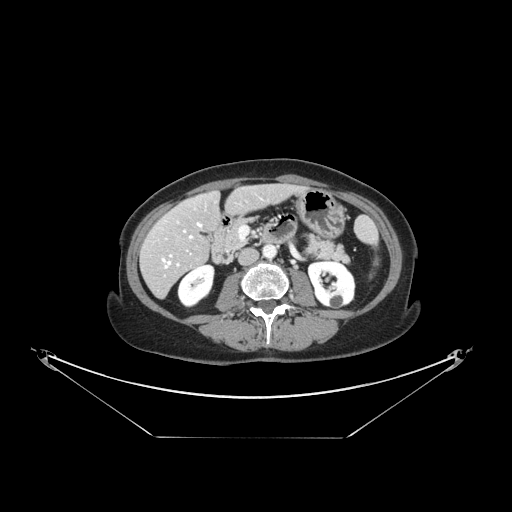
Contrast-enhanced abdominal CT, one axial slice. Position 53 of 148 along the scan axis. Reconstruction kernel STANDARD. Intravenous contrast given. Soft-tissue window (W 400 / L 40 HU). 2.5 mm slice thickness. 512 × 512 image matrix, field of view 500 × 500 mm. Female patient, age 73 years. Case-level facts recorded for this patient, not image findings: diagnosis: colorectal cancer liver metastases, imaged before liver resection; multiple liver metastases: no.
Outlined on this slice (outlined manually by an expert reader):
- hepatic veins: bounding box (x1, y1, x2, y2) in pixels: (163, 223, 202, 268)
- liver: (143, 184, 296, 296)
- planned liver remnant (the part of the liver to remain after resection): (163, 185, 296, 248)